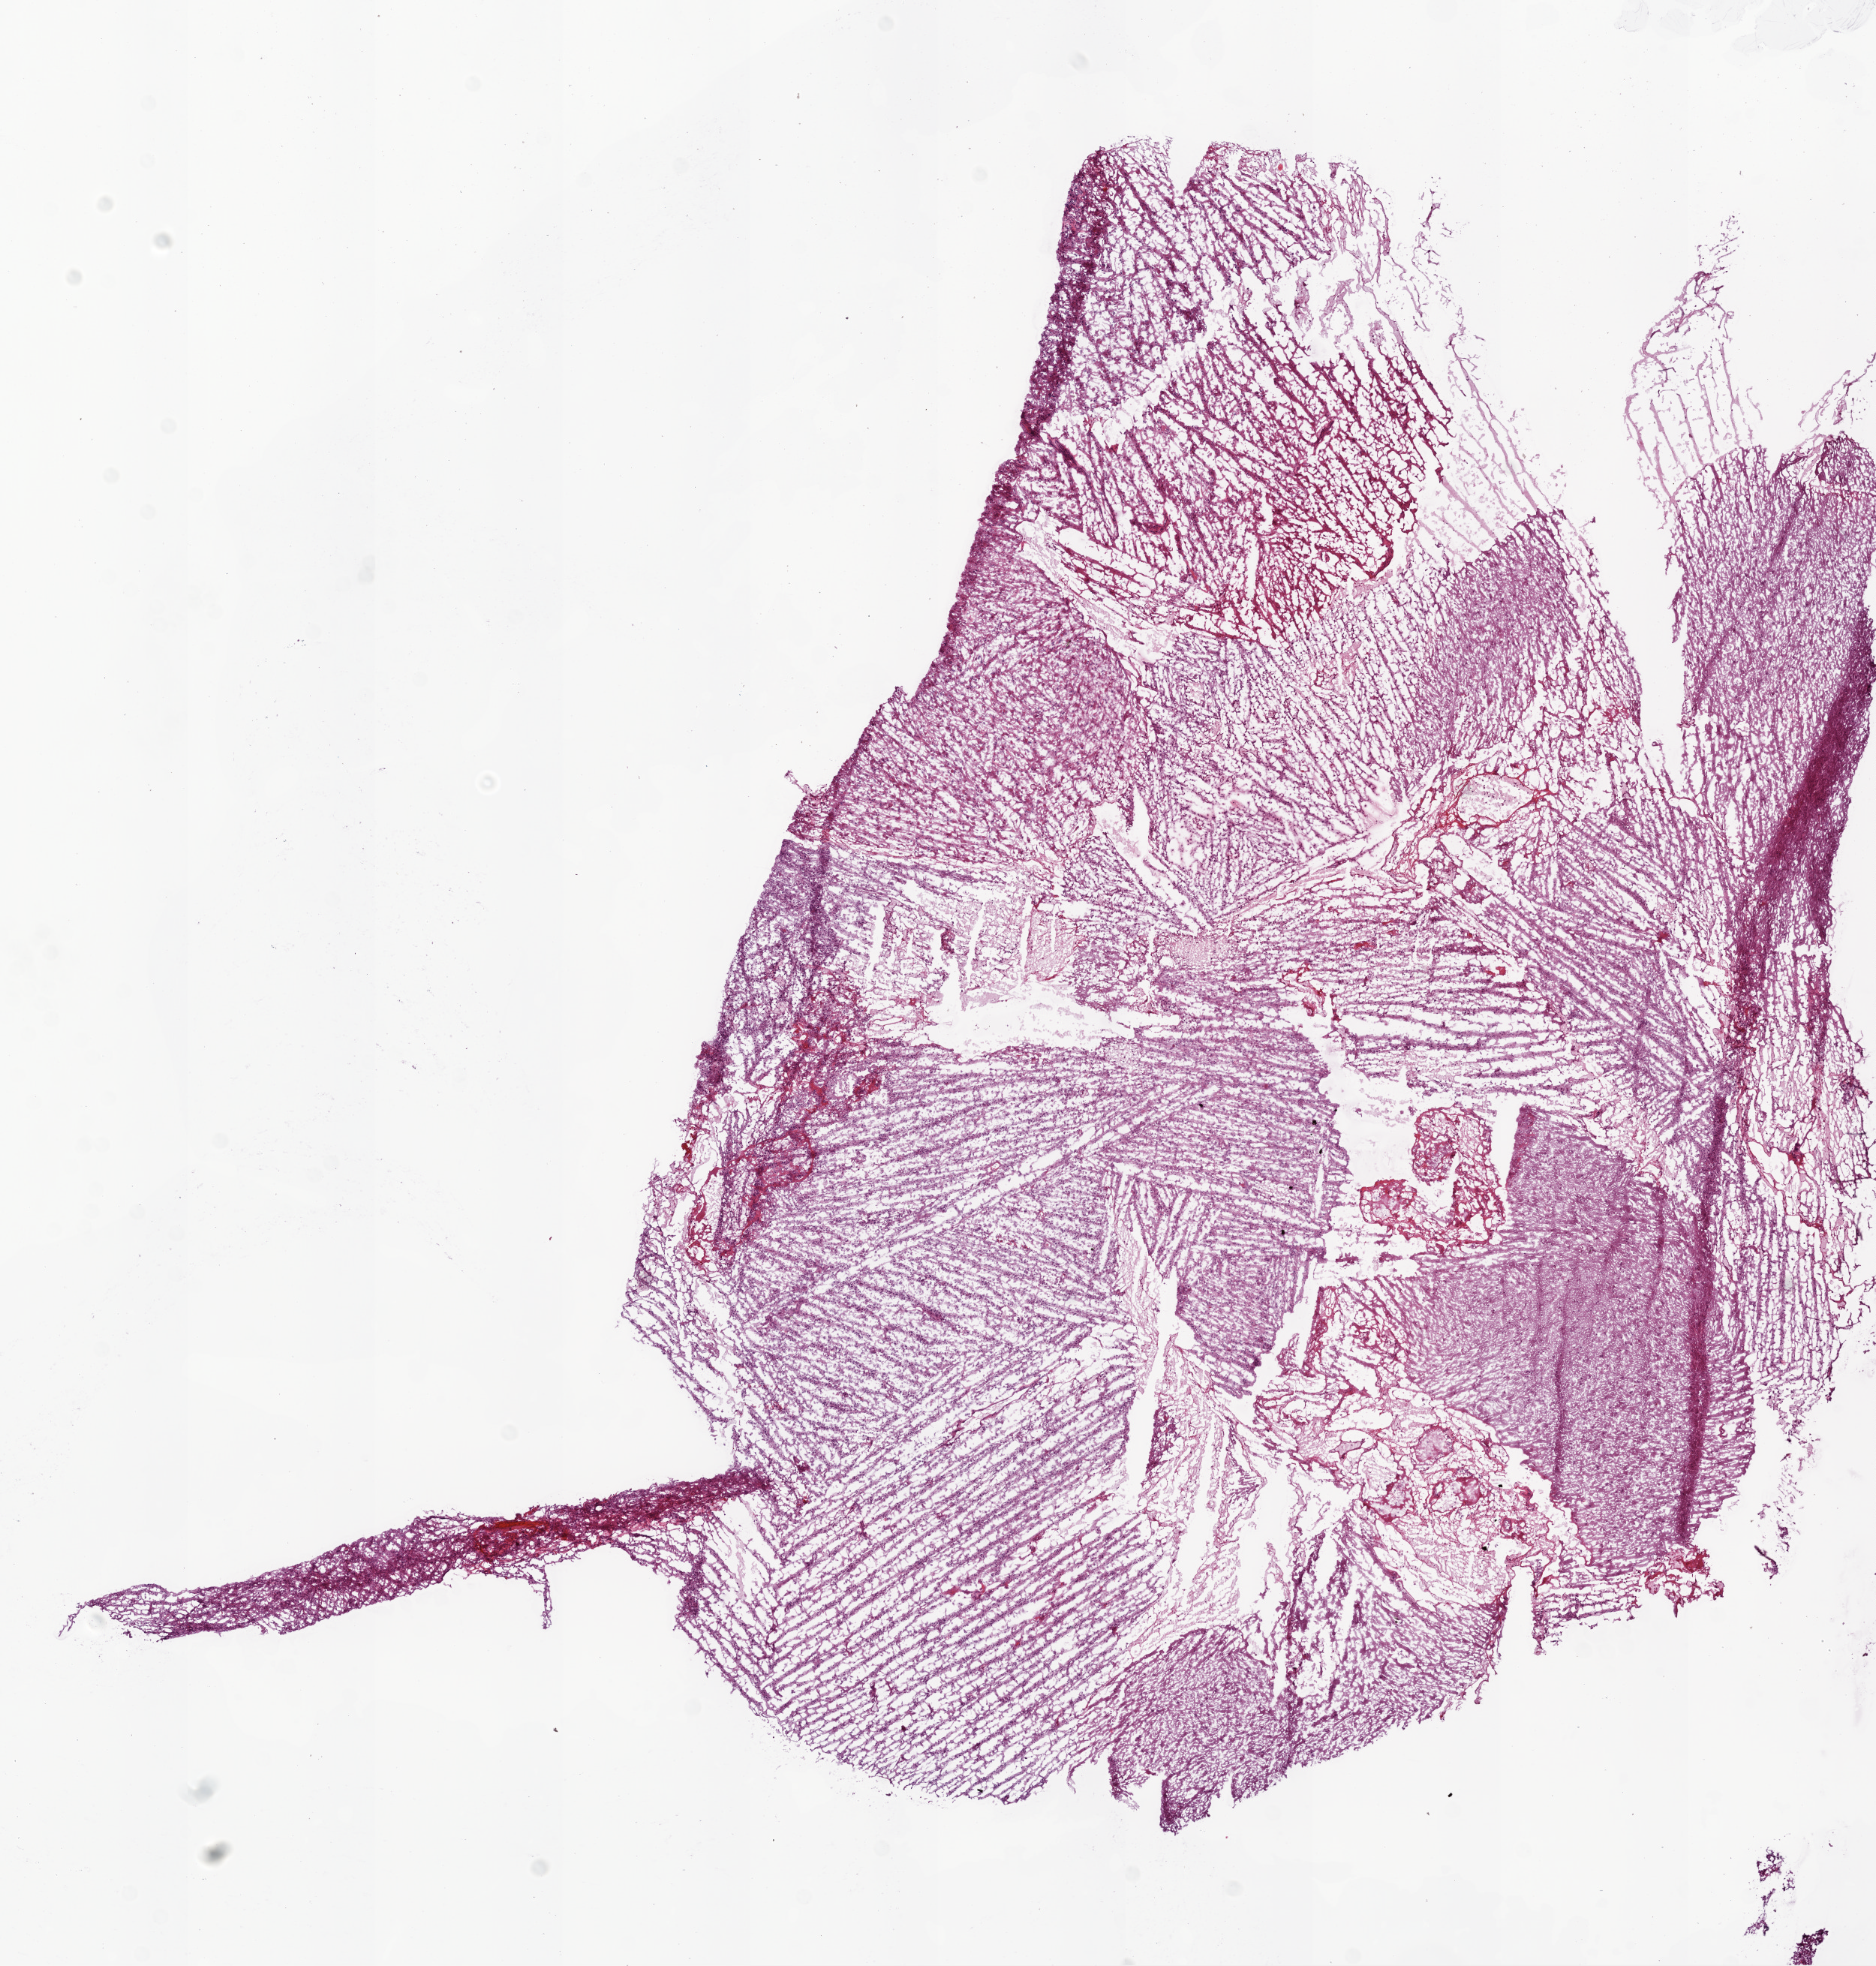
Whole-slide histology image, Hematoxylin and eosin (H&E) stained, whole scanned area (about 10.0 x 10.5 mm) shown as a low-resolution overview, frozen section from the bottom of the tissue portion, sample: primary tumour, brain. Patient: male, age at initial diagnosis 61 years. Pathologist review of this section (percent, as recorded): tumour cells 85%, tumour nuclei 85%, normal cells 10%, stromal cells 5%, necrosis 0%.
* pathologic diagnosis: Glioblastoma